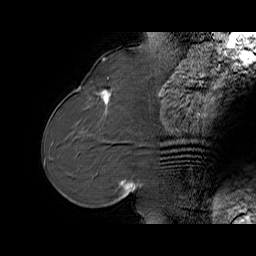
Breast MRI (dynamic contrast-enhanced), one sagittal slice. Slice 25 of 65 in the series (ordered by position). Dynamic contrast-enhanced series, time point 2 of 6 at this slice position (early post-contrast). 1.5 T. TE 5.7 ms, TR 32.9 ms. 4 mm slice thickness. 256 × 256 image matrix, field of view 230 × 230 mm. Female patient. Case-level facts recorded for this patient, not image findings: setting: breast cancer imaged before/during neoadjuvant chemotherapy; receptor status: HER2-positive.
Annotated regions visible in this slice (semi-automatic segmentation, software-assisted and operator-edited):
- analysis volume of interest (the breast-tissue region the enhancement analysis was run in; not a lesion): bounding box (x1, y1, x2, y2) in pixels: (76, 77, 125, 128)
- tumour enhancement mask (voxels above the 100 % enhancement threshold inside the analysis volume of interest): (100, 90, 108, 112)